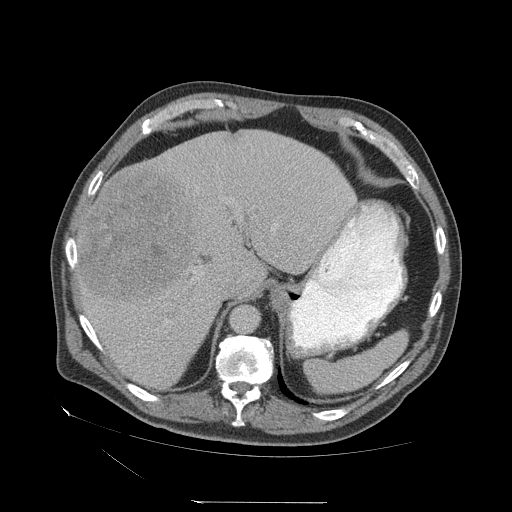
Contrast-enhanced abdominal CT (liver protocol), one axial slice; position 46 of 83 along the scan axis; reconstruction kernel STANDARD; 140 kVp; soft-tissue window (W 400 / L 40 HU); 2.5 mm slice thickness; 512 × 512 image matrix, field of view 460 × 460 mm. From the clinical record (not read from this slice): diagnosis: hepatocellular carcinoma (patient treated with transarterial chemoembolisation; whether this scan precedes or follows treatment is not stated here); TNM stage (as recorded): Stage-I; Child-Pugh class: A.
Outlined on this slice (semi-automatically segmented with operator editing):
- liver parenchyma outside the tumour (the mass and vessels are separate outlines, so this box may not span the whole liver): box from (x=76, y=130) to (x=356, y=388) px
- mass: (x=81, y=166)–(x=201, y=307)
- liver vessels: (x=90, y=224)–(x=277, y=349)